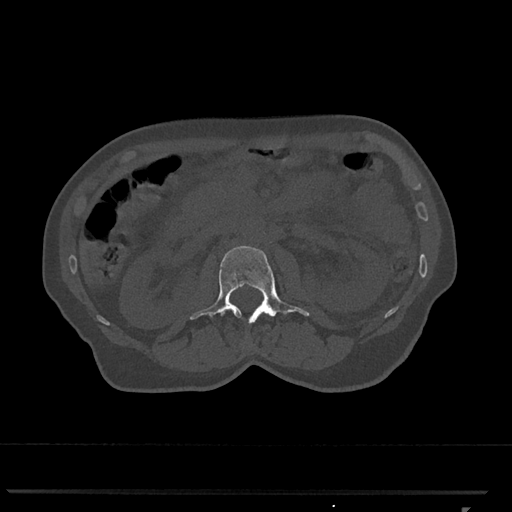
CT including the spine, one axial slice; slice 345 of 793 in the series (ordered by position); reconstruction kernel Br40s/3; 120 kVp; bone window (W 1800 / L 400 HU); 512 × 512 image matrix, field of view 380 × 380 mm. Female patient, age 62 years. From the clinical record (not read from this slice): primary cancer: renal.
Outlined on this slice (semi-automatic segmentation, software-assisted and operator-edited):
- L2 vertebra: bounding box <190,246,310,324> (left, top, right, bottom; pixels)